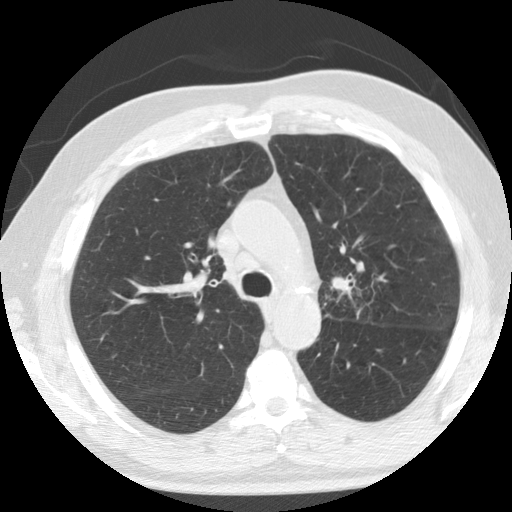
Axial slice from a low-dose chest CT screening exam; second screening round (one year after baseline); lung window (W 1500 / L -600 HU); 2.5 mm slice thickness; standard (soft-tissue) reconstruction kernel (STANDARD); slice 43 of 133 in the series. Male participant, aged 74 years at enrolment.
Expert reader's lesion annotation, bounding box (x1, y1, x2, y2) in pixels: (305, 259, 371, 323). Screening reader's record for this exam: no non-calcified nodule ≥4 mm recorded. Official screen result: positive, other. Lung cancer was diagnosed 274 days after this screen: non-small cell carcinoma, left upper lobe, poorly differentiated (G3), stage IIB (AJCC 6th edition).